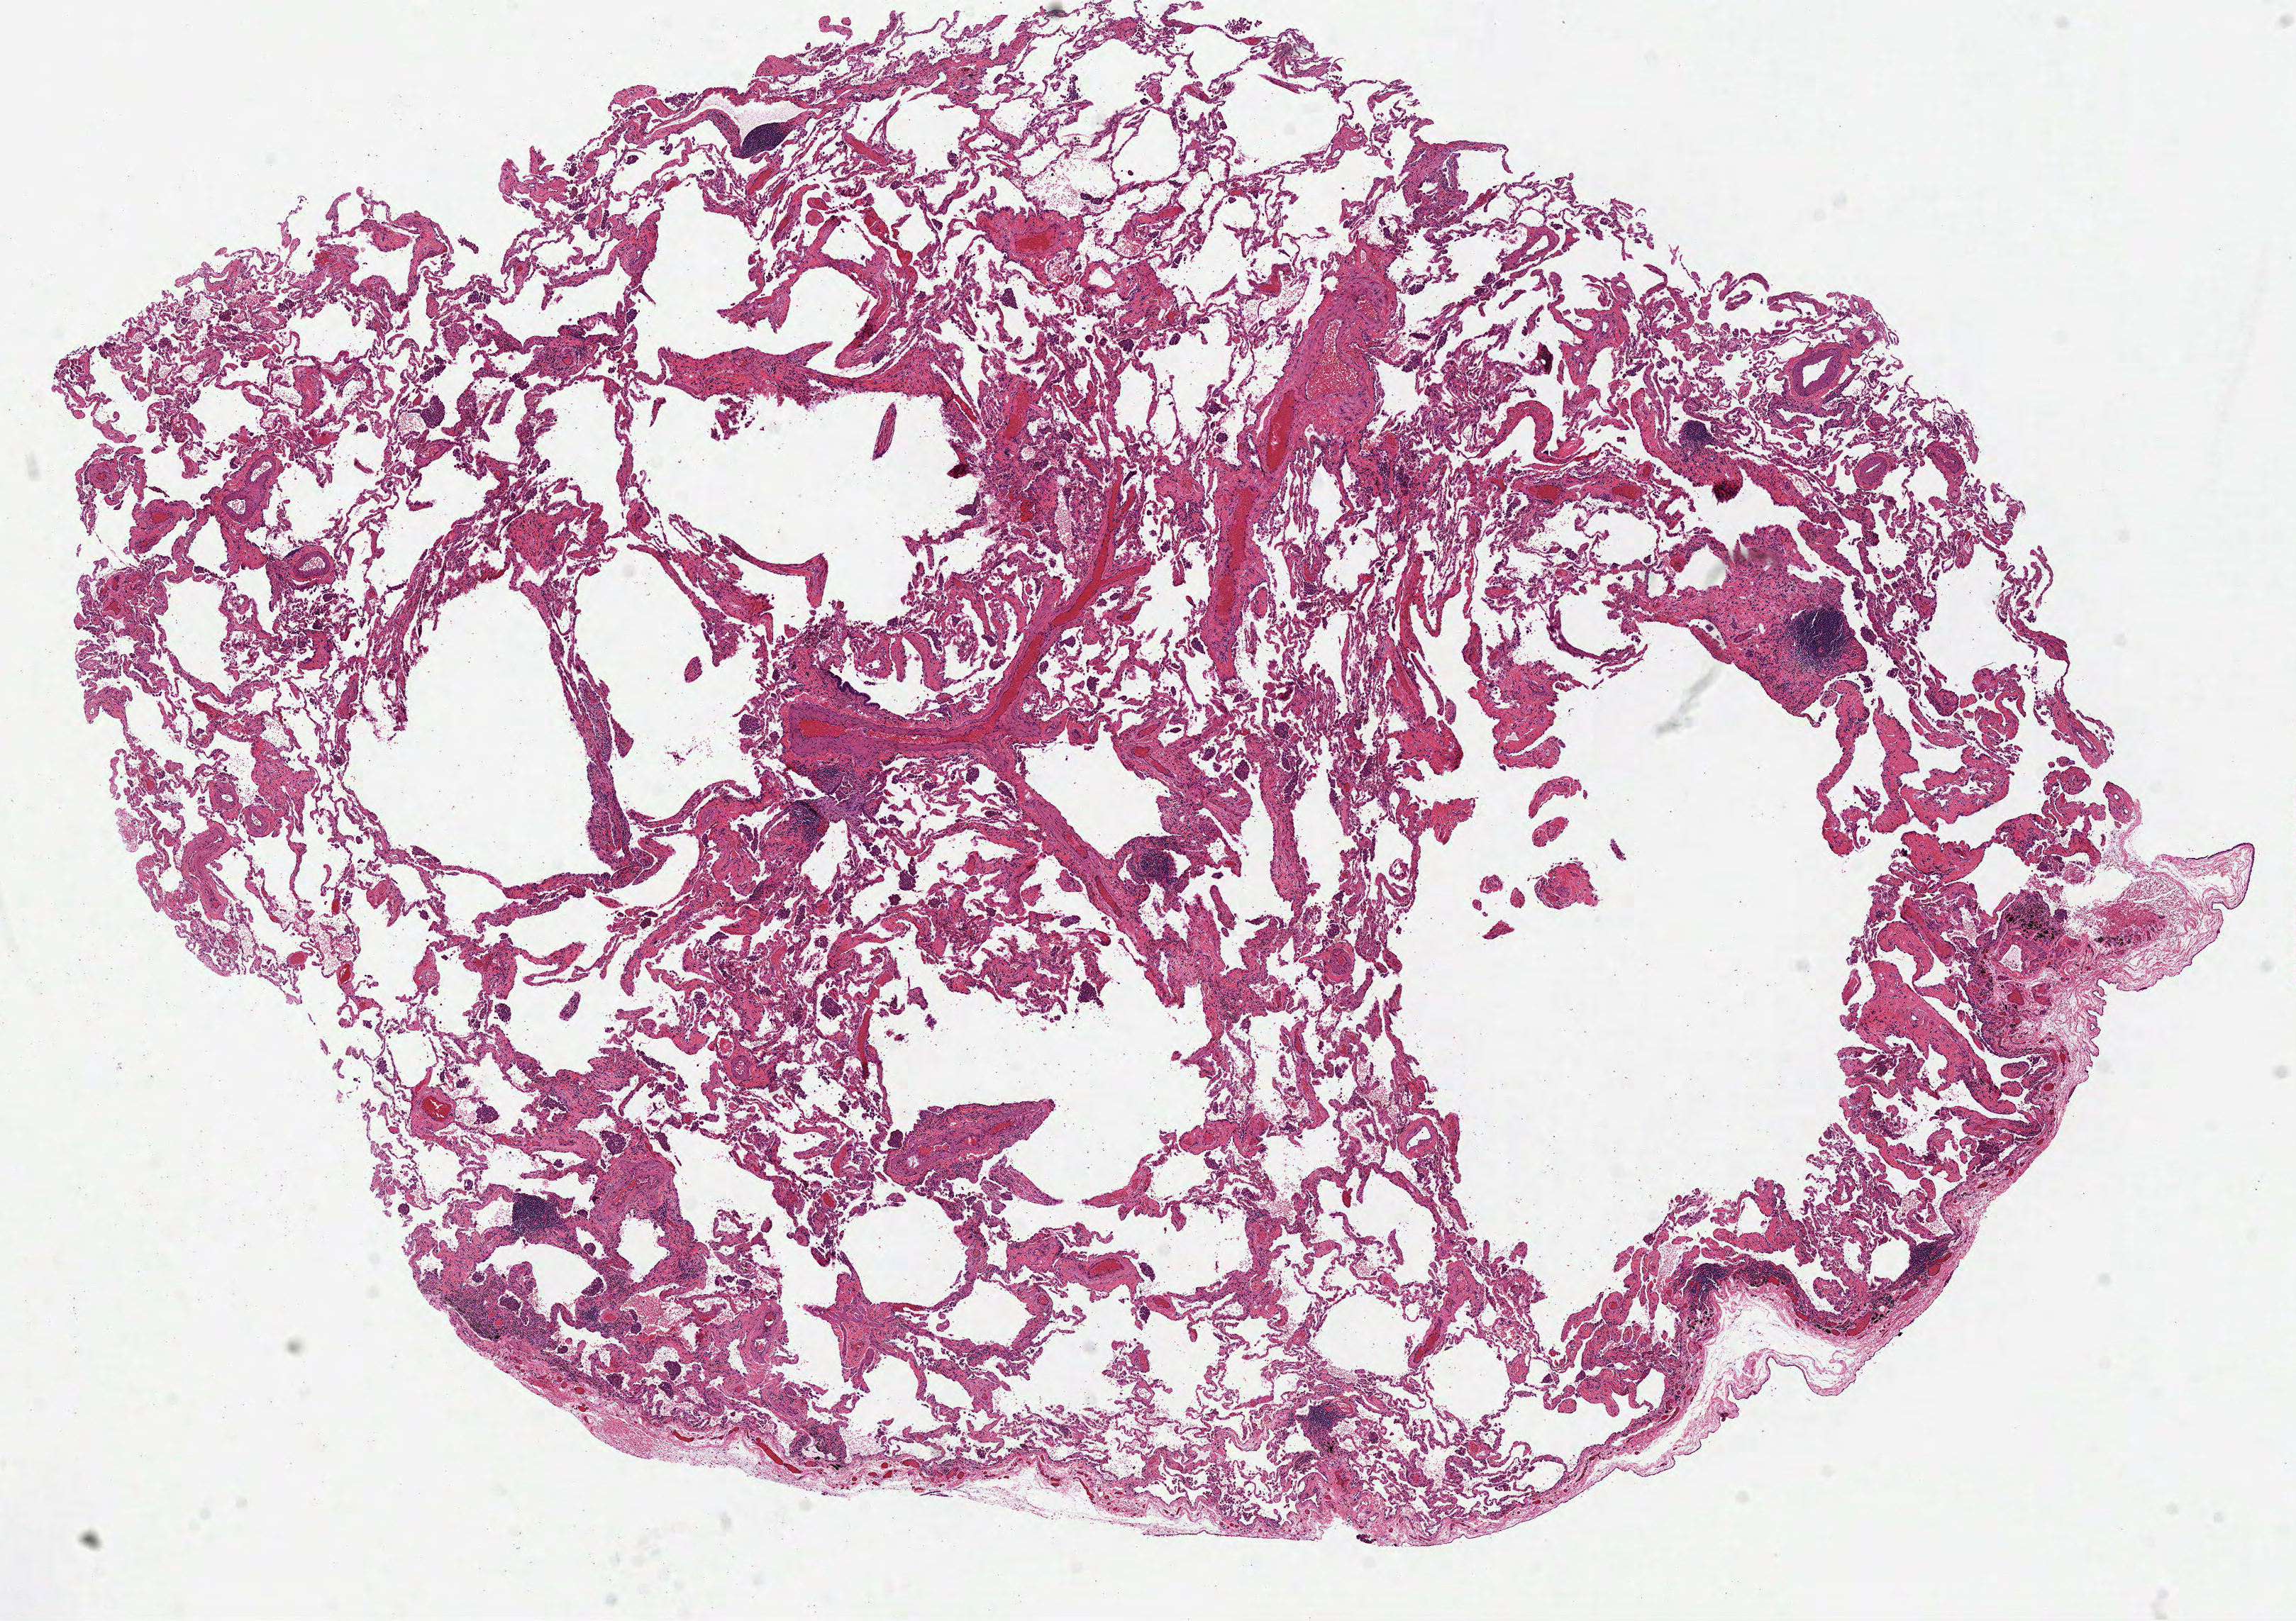
Digitized H&E-stained tissue section (whole slide) — a low-resolution overview of the entire scanned area, about 13.1 x 9.2 mm (from a 40x scan). Frozen section. Solid tissue normal (non-tumour tissue) sample from the lung. Patient: male, age at initial diagnosis 70 years.
This section: solid tissue normal (non-tumour) sample from the same patient. Patient diagnosis: Basaloid squamous cell carcinoma (lower lobe, lung).